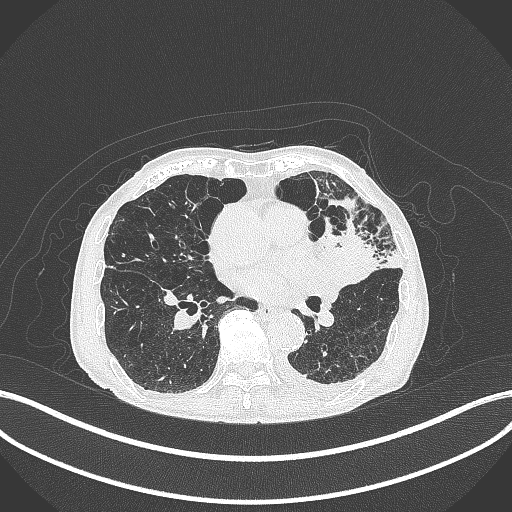
Chest CT, one axial slice. Reconstruction kernel B70f. 120 kVp. Lung window (W 1500 / L -600 HU). 512 × 512 image matrix. Patient: male, 90 years or older. Case-level facts recorded for this patient, not image findings: clinical TNM (as recorded): T2b N1 M0.
Annotated regions visible in this slice (rectangle marked by the reading radiologist):
- lung tumour (recorded histology: squamous cell carcinoma): bounding box [x1, y1, x2, y2] px = [311, 228, 379, 282]